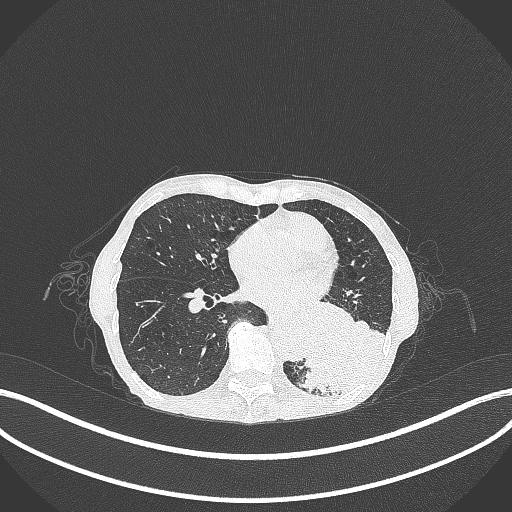
Chest CT, one axial slice. Slice 108 of 347 in the series (ordered by position). Reconstruction kernel B70f. Lung window (W 1500 / L -600 HU). 1 mm slice thickness. 512 × 512 image matrix, field of view 400 × 400 mm. Patient: female, 70 years. Case-level facts recorded for this patient, not image findings: clinical TNM (as recorded): T3 N0 M0; histopathological grade: G3.
Structures marked on this image (rectangle marked by the reading radiologist):
- lung tumour (recorded histology: small cell carcinoma): bounding box [x1, y1, x2, y2] px = [291, 302, 394, 396]